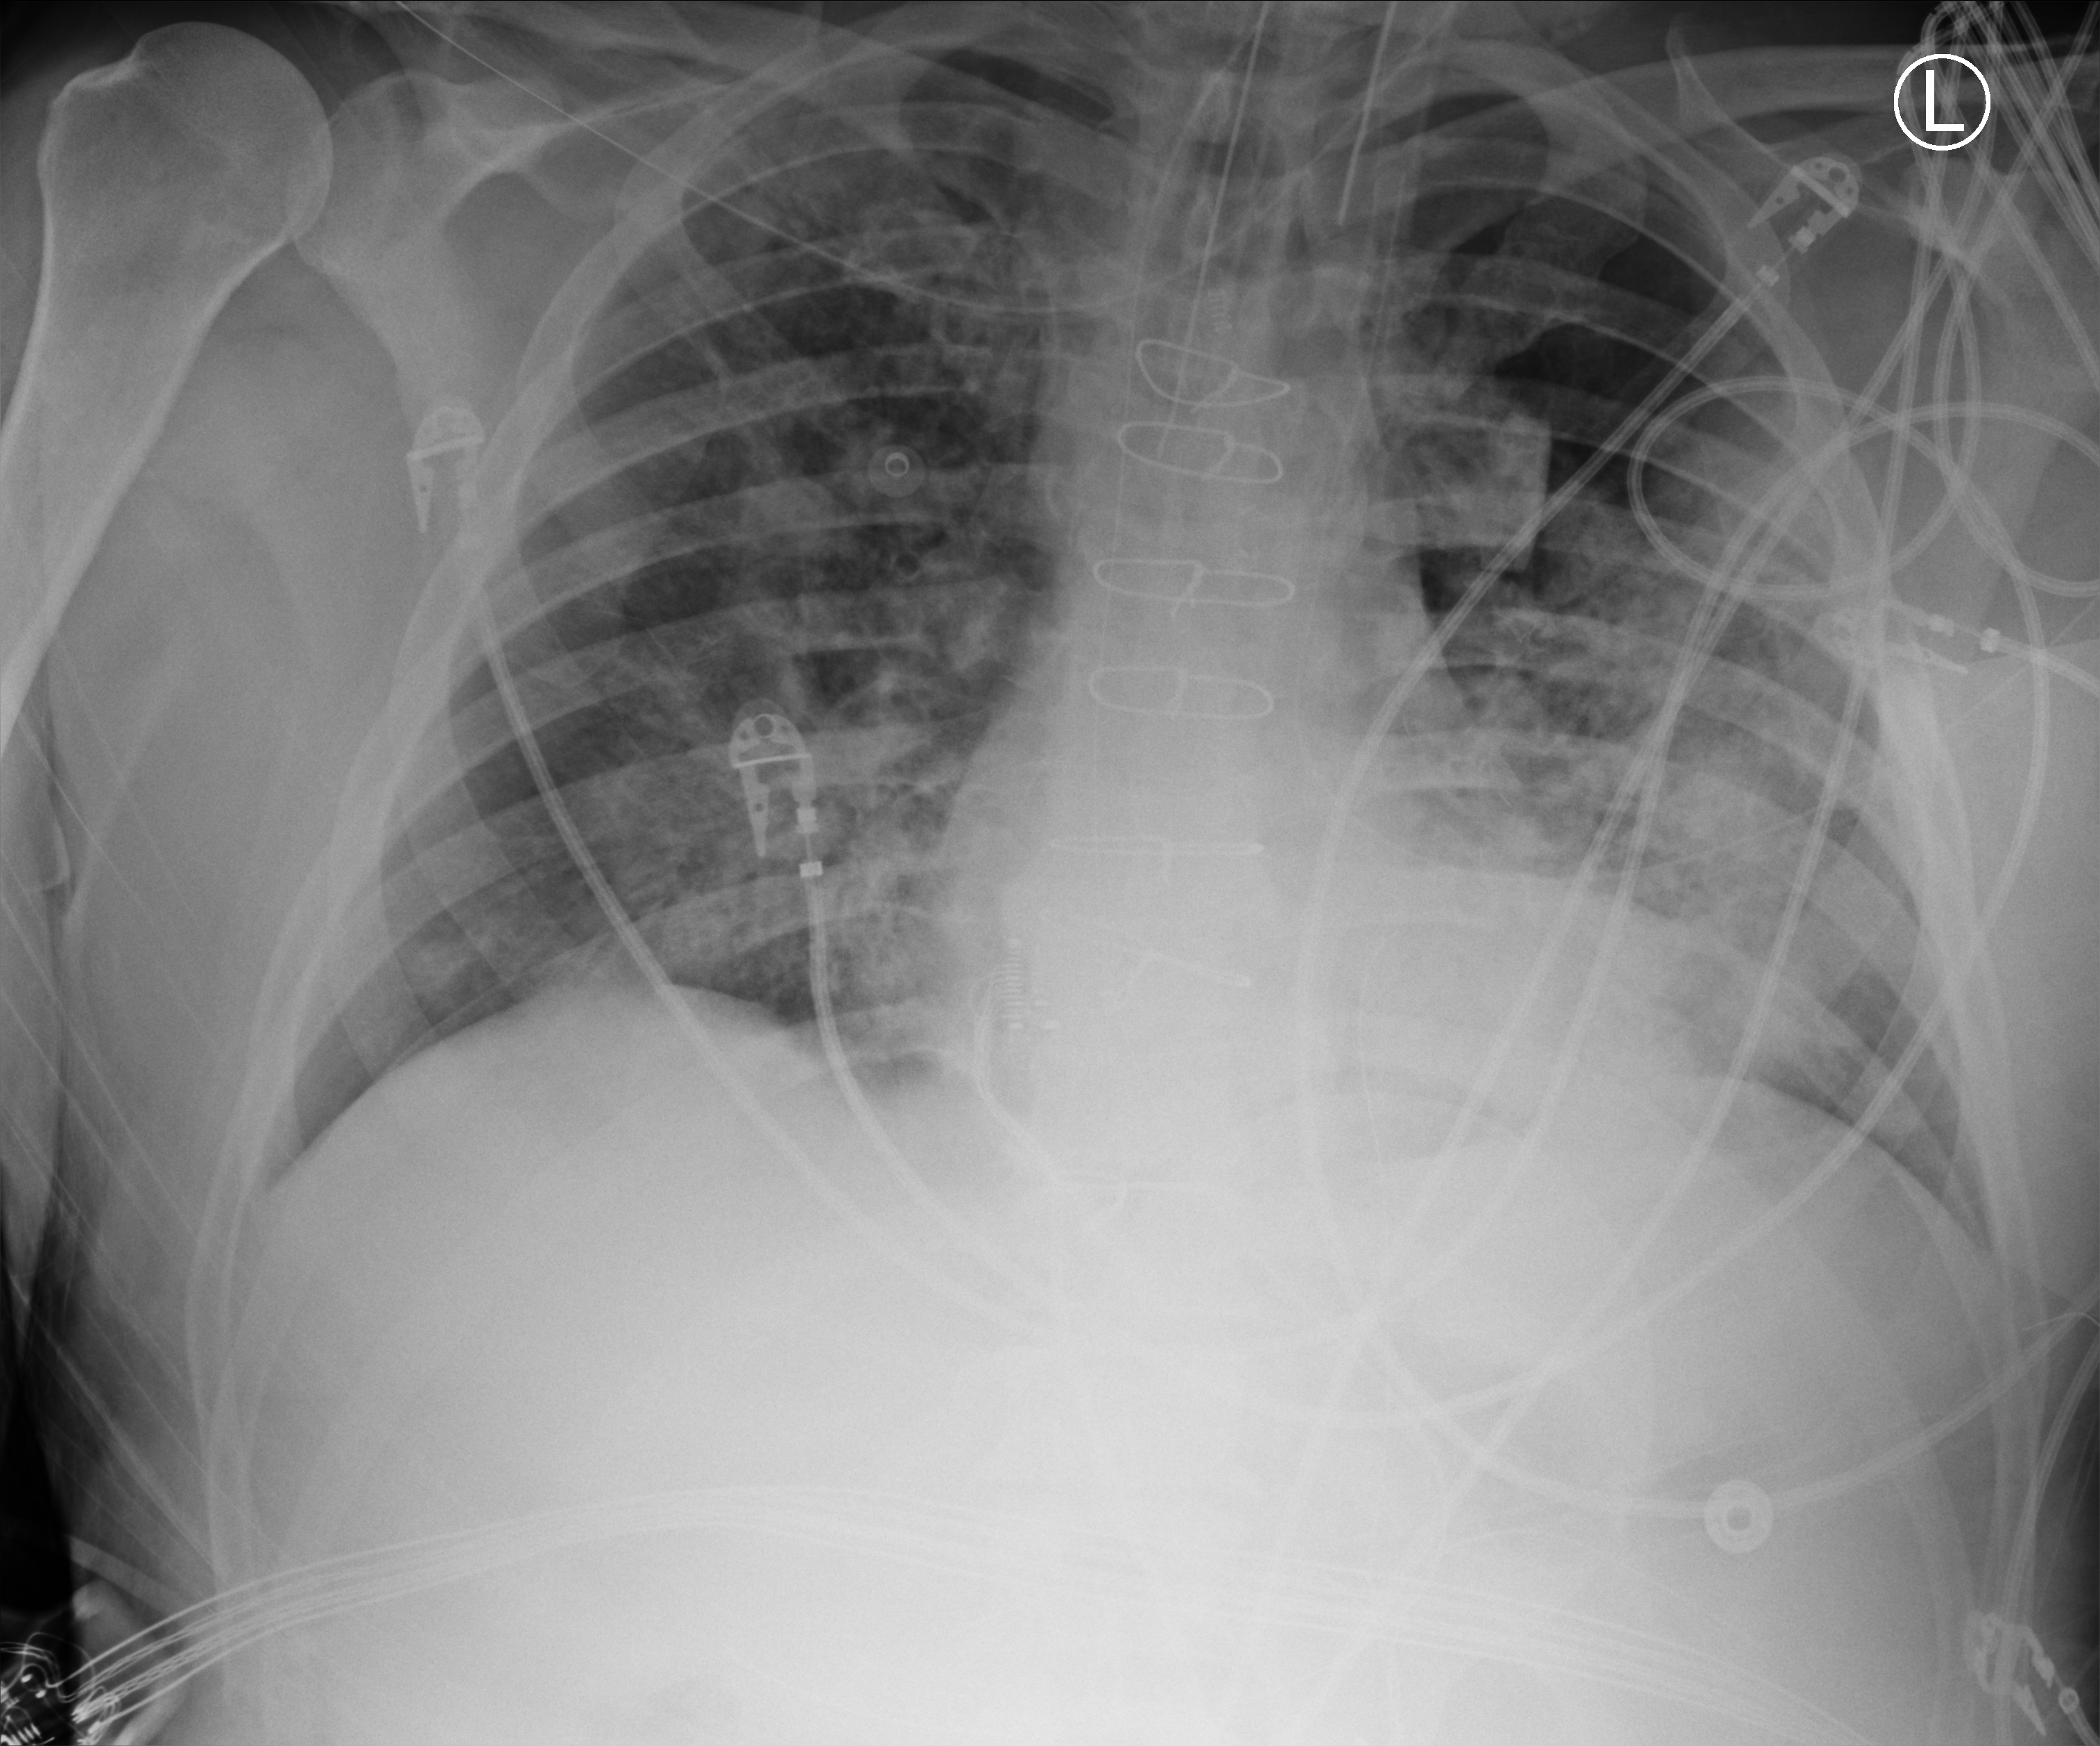
Chest X-ray (portable); anteroposterior (AP) projection. Male patient hospitalised with COVID-19, age 60–74 years.
From the hospital-stay record, not from the radiograph (when in the stay this image was taken is not recorded): length of hospital stay: 44 days.